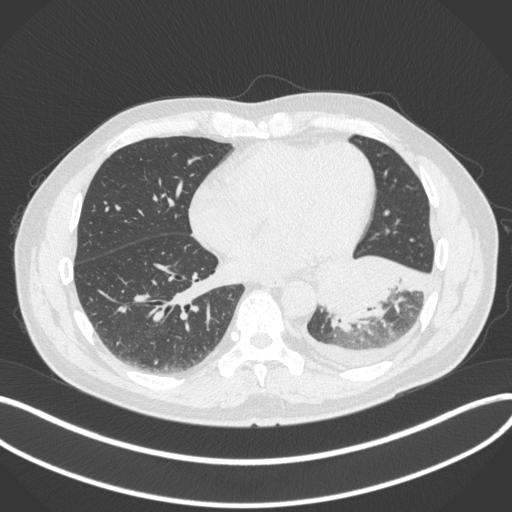
Chest CT, one axial slice. Position 133 of 350 along the scan axis. Reconstruction kernel B31f. Lung window (W 1500 / L -600 HU). 512 × 512 image matrix. Male patient, age 58 years. From the clinical record (not read from this slice): clinical TNM (as recorded): T3 N1 M1b; histopathological grade: G3.
Structures marked on this image (bounding box drawn by a radiologist):
- lung tumour (recorded histology: small cell carcinoma): bounding box <314,246,435,332> (left, top, right, bottom; pixels)